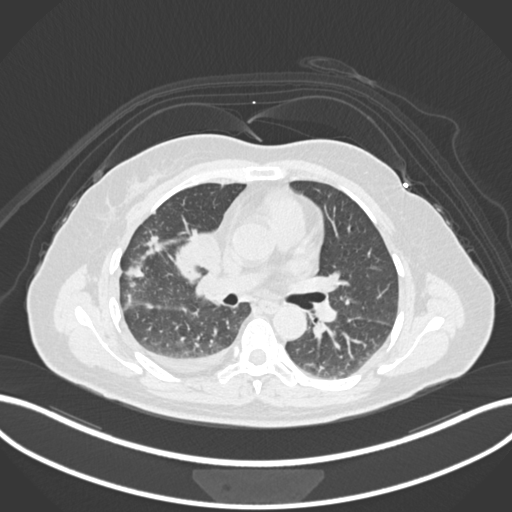
Chest CT, one axial slice; slice 77 of 172 in the series (ordered by position); lung window (W 1500 / L -600 HU); 512 × 512 image matrix, field of view 400 × 400 mm. Patient: female, 52 years. Case-level facts recorded for this patient, not image findings: clinical TNM (as recorded): T3 N1 M1.
Structures marked on this image (bounding box drawn by a radiologist):
- lung tumour (recorded histology: adenocarcinoma): bounding box [x1, y1, x2, y2] px = [174, 227, 224, 275]